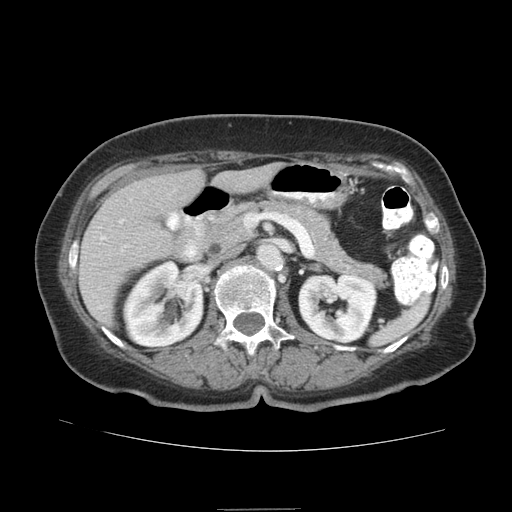
Contrast-enhanced abdominal CT (liver protocol), one axial slice. Slice 36 of 95 in the series (ordered by position). Reconstruction kernel STANDARD. 140 kVp. Soft-tissue window (W 400 / L 40 HU). 2.5 mm slice thickness. 512 × 512 image matrix, field of view 360 × 360 mm. Case-level facts recorded for this patient, not image findings: diagnosis: hepatocellular carcinoma (patient treated with transarterial chemoembolisation; whether this scan precedes or follows treatment is not stated here); TNM stage (as recorded): Stage-IVA; Child-Pugh class: B.
Structures marked on this image (semi-automatically segmented with operator editing):
- liver parenchyma outside the tumour (the mass and vessels are separate outlines, so this box may not span the whole liver): bounding box (x1, y1, x2, y2) in pixels: (78, 162, 281, 322)
- liver vessels: (101, 237, 105, 240)